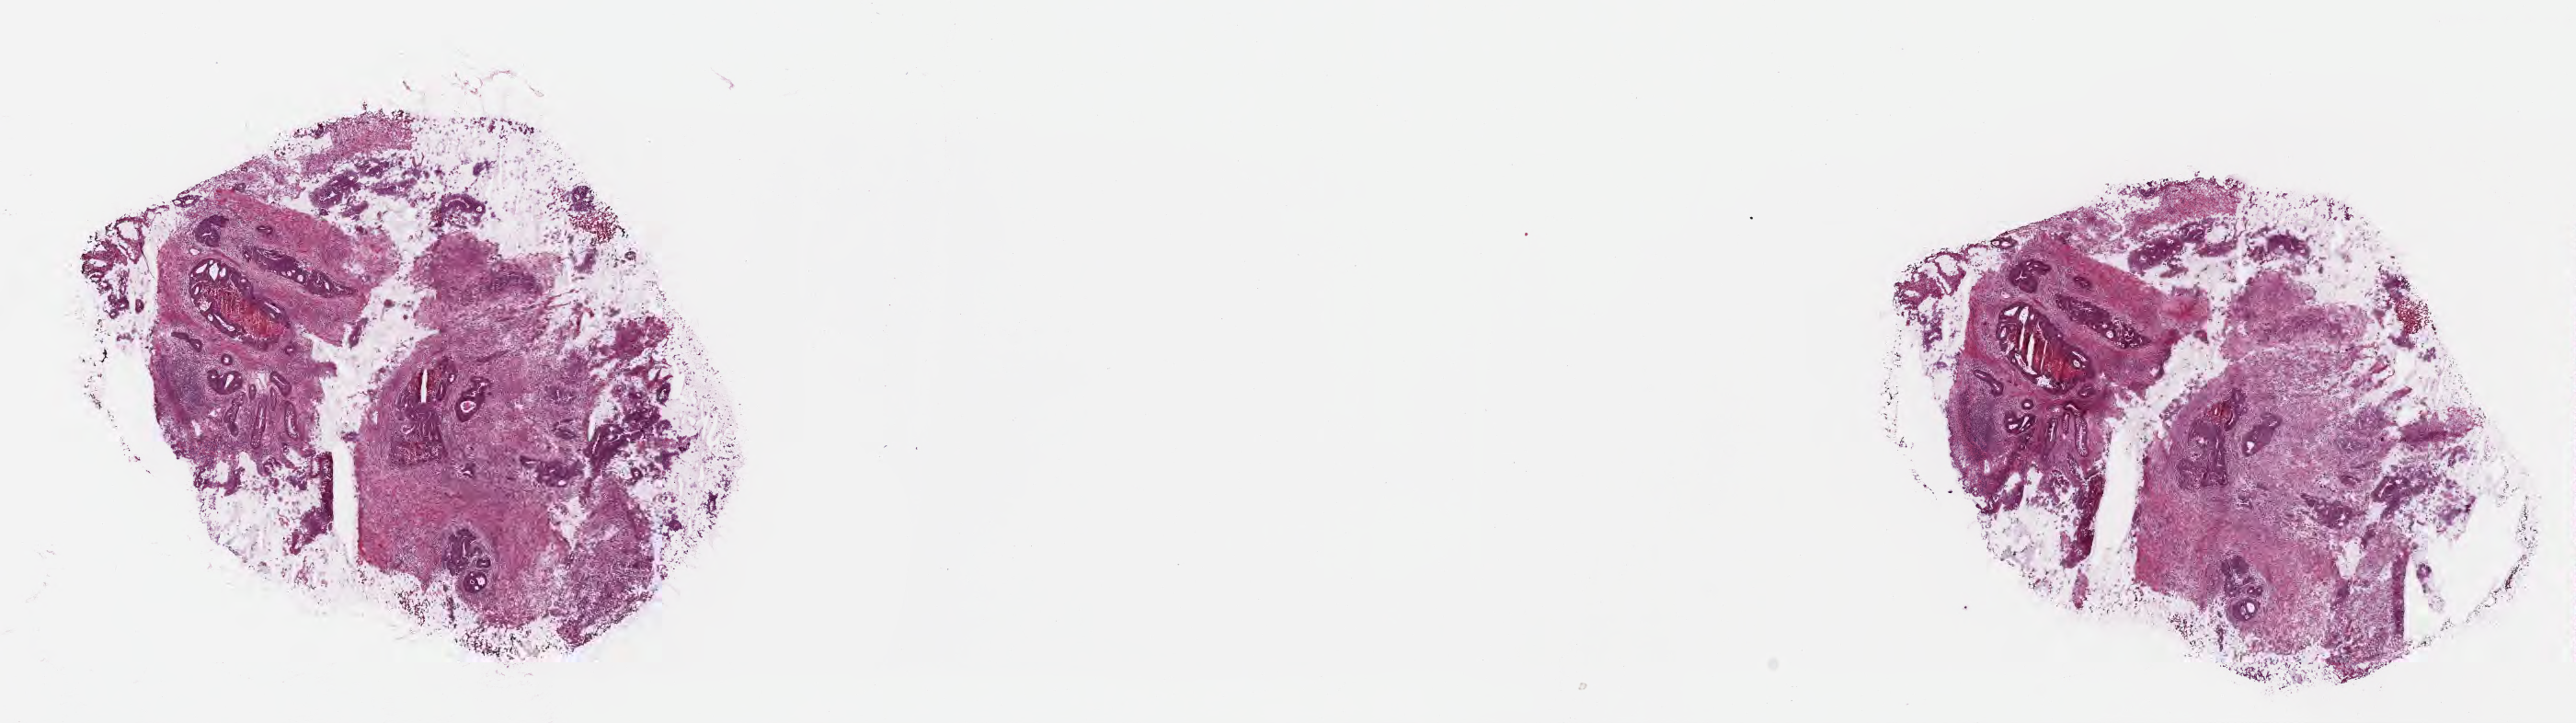
Haematoxylin and eosin whole-slide image — whole scanned area (about 22.6 x 6.4 mm) shown as a low-resolution overview. Frozen section (tissue freezing medium). Specimen: primary tumor. Anatomic site: sigmoid colon. Patient: male, age at initial diagnosis 54 years. Tumor grade: G2 (moderately differentiated). Slide review estimates, as recorded: tumor cells 70%, tumor nuclei 70%, stromal cells 25%, necrosis 2%, normal cells 3%. Inflammatory infiltration, as recorded: lymphocyte infiltration 5%, monocyte infiltration 6%, neutrophil infiltration 8%.
AJCC pathologic stage: Stage IIIB. Diagnosis: Adenocarcinoma, NOS.